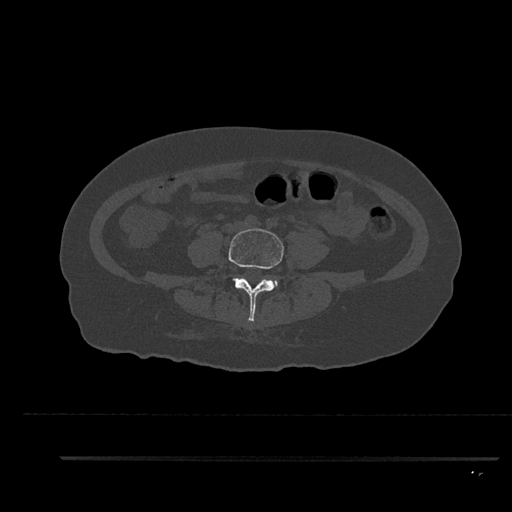
CT including the spine, one axial slice; slice 10 of 797 in the series (ordered by position); reconstruction kernel Br40s/3; 120 kVp; bone window (W 1800 / L 400 HU); 0.5 mm slice thickness; 512 × 512 image matrix, field of view 408 × 408 mm. Patient: female, 44 years. Case-level facts recorded for this patient, not image findings: primary cancer: renal.
Annotated regions visible in this slice (semi-automatically segmented with operator editing):
- L4 vertebra: bounding box (x1, y1, x2, y2) in pixels: (228, 228, 284, 322)